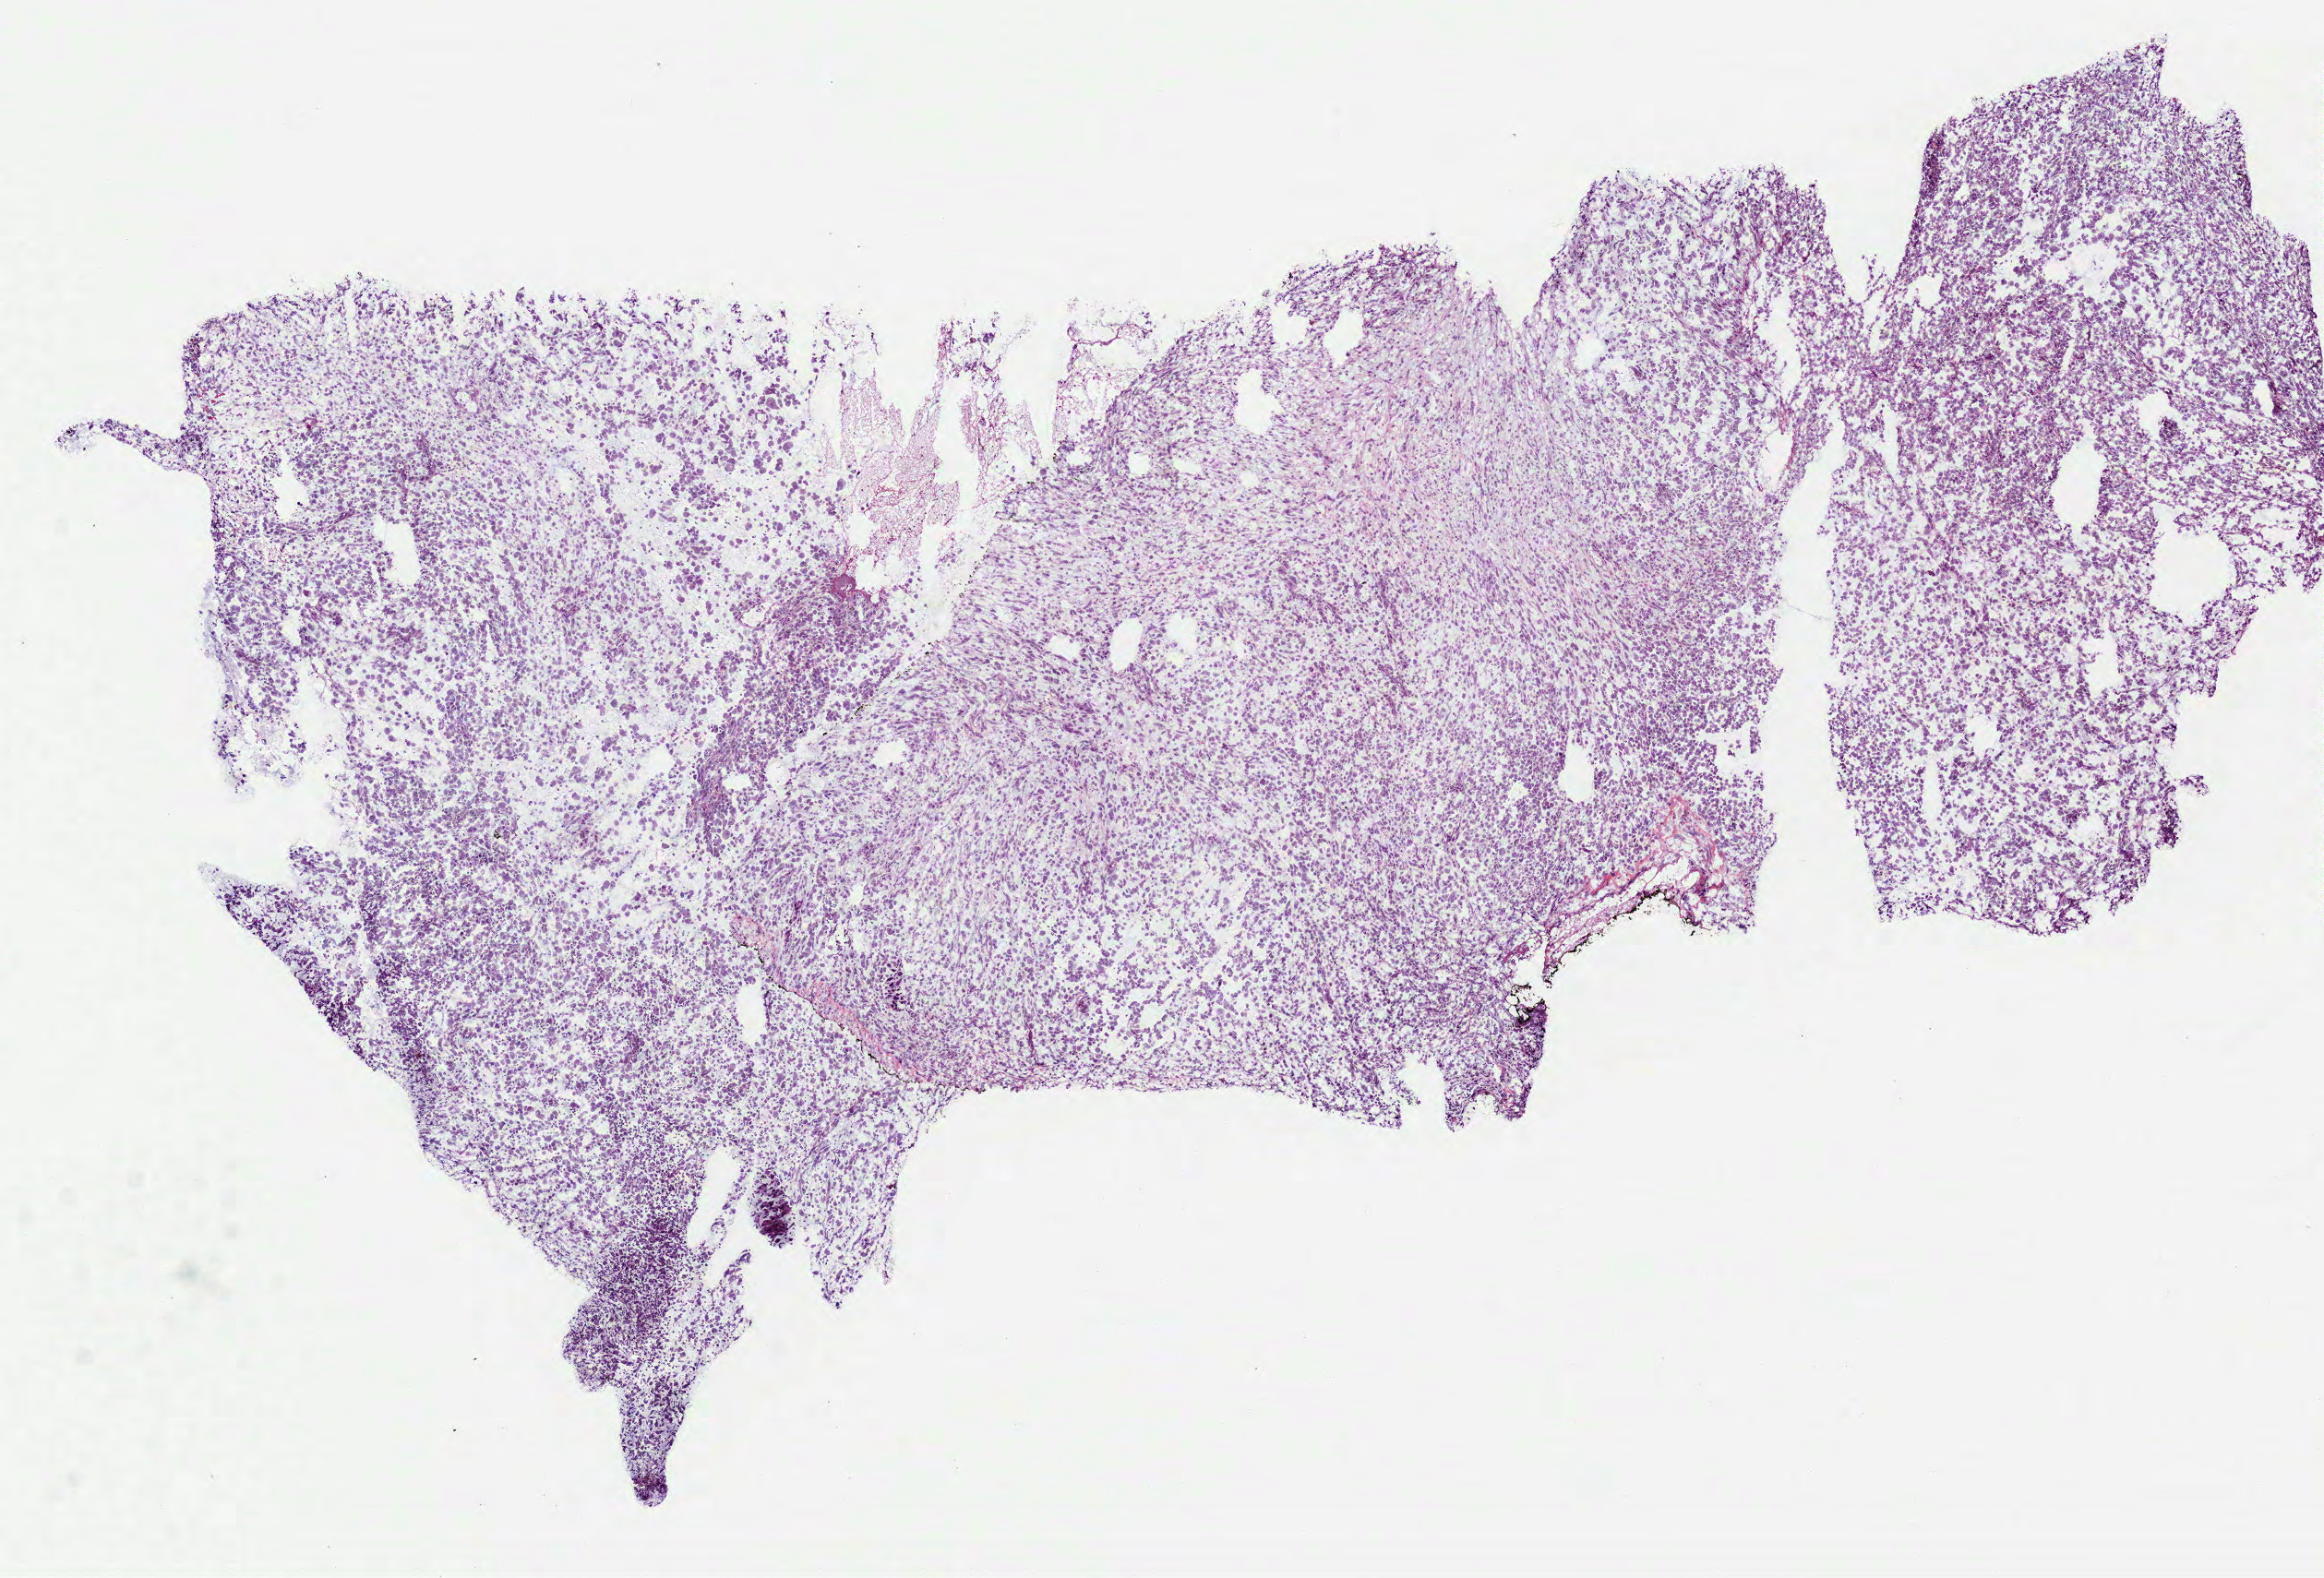
Digitized Hematoxylin and eosin (H&E) stained tissue section (whole slide), whole scanned area (about 10.2 x 6.9 mm, acquisition: 40x scan) shown as a low-resolution overview; frozen section from the top of the tissue portion; primary tumour sample from the mesothelium. Patient: male, age at initial diagnosis 71 years. Slide review estimates, as recorded: tumour cells 100%, tumour nuclei 80%, normal cells 0%, stromal cells 0%, necrosis 0%. Infiltration values recorded for this section: lymphocyte infiltration 3%, monocyte infiltration 0%, neutrophil infiltration 0%.
* AJCC pathologic stage: IB (7th edition)
* laterality: right
* diagnosis: Mesothelioma, biphasic, malignant